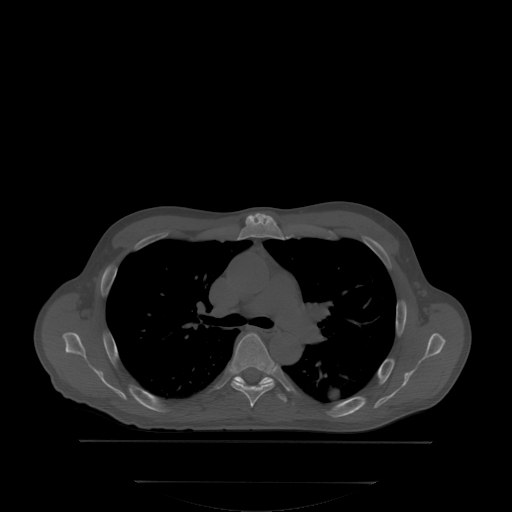
CT including the spine, one axial slice; slice 245 of 350 in the series (ordered by position); bone window (W 1800 / L 400 HU); 512 × 512 image matrix. Male patient, age 58 years. Case-level facts recorded for this patient, not image findings: primary cancer: prostate; vertebrae with lytic lesions (as recorded): L1.
Outlined on this slice (semi-automatic segmentation, software-assisted and operator-edited):
- T5 vertebra: box from (x=231, y=333) to (x=275, y=407) px
- T6 vertebra: (x=232, y=377)–(x=285, y=400)